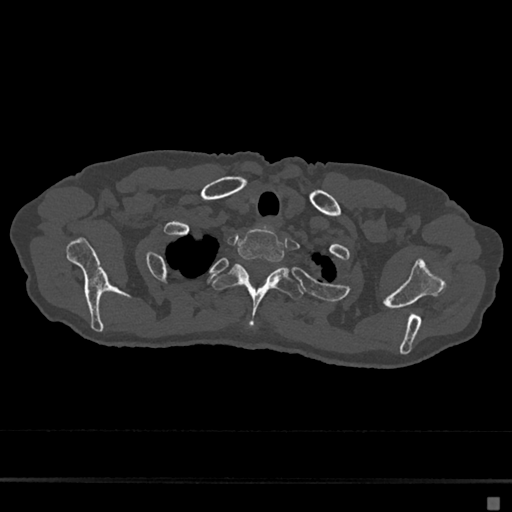
CT including the spine, one axial slice; position 589 of 797 along the scan axis; 120 kVp; bone window (W 1800 / L 400 HU); 0.5 mm slice thickness; 512 × 512 image matrix, field of view 360 × 360 mm. Patient: female, 68 years. From the clinical record (not read from this slice): primary cancer: renal.
Annotated regions visible in this slice (semi-automatically segmented with operator editing):
- T1 vertebra: bounding box (x1, y1, x2, y2) in pixels: (237, 227, 285, 263)
- T2 vertebra: (212, 263, 303, 328)